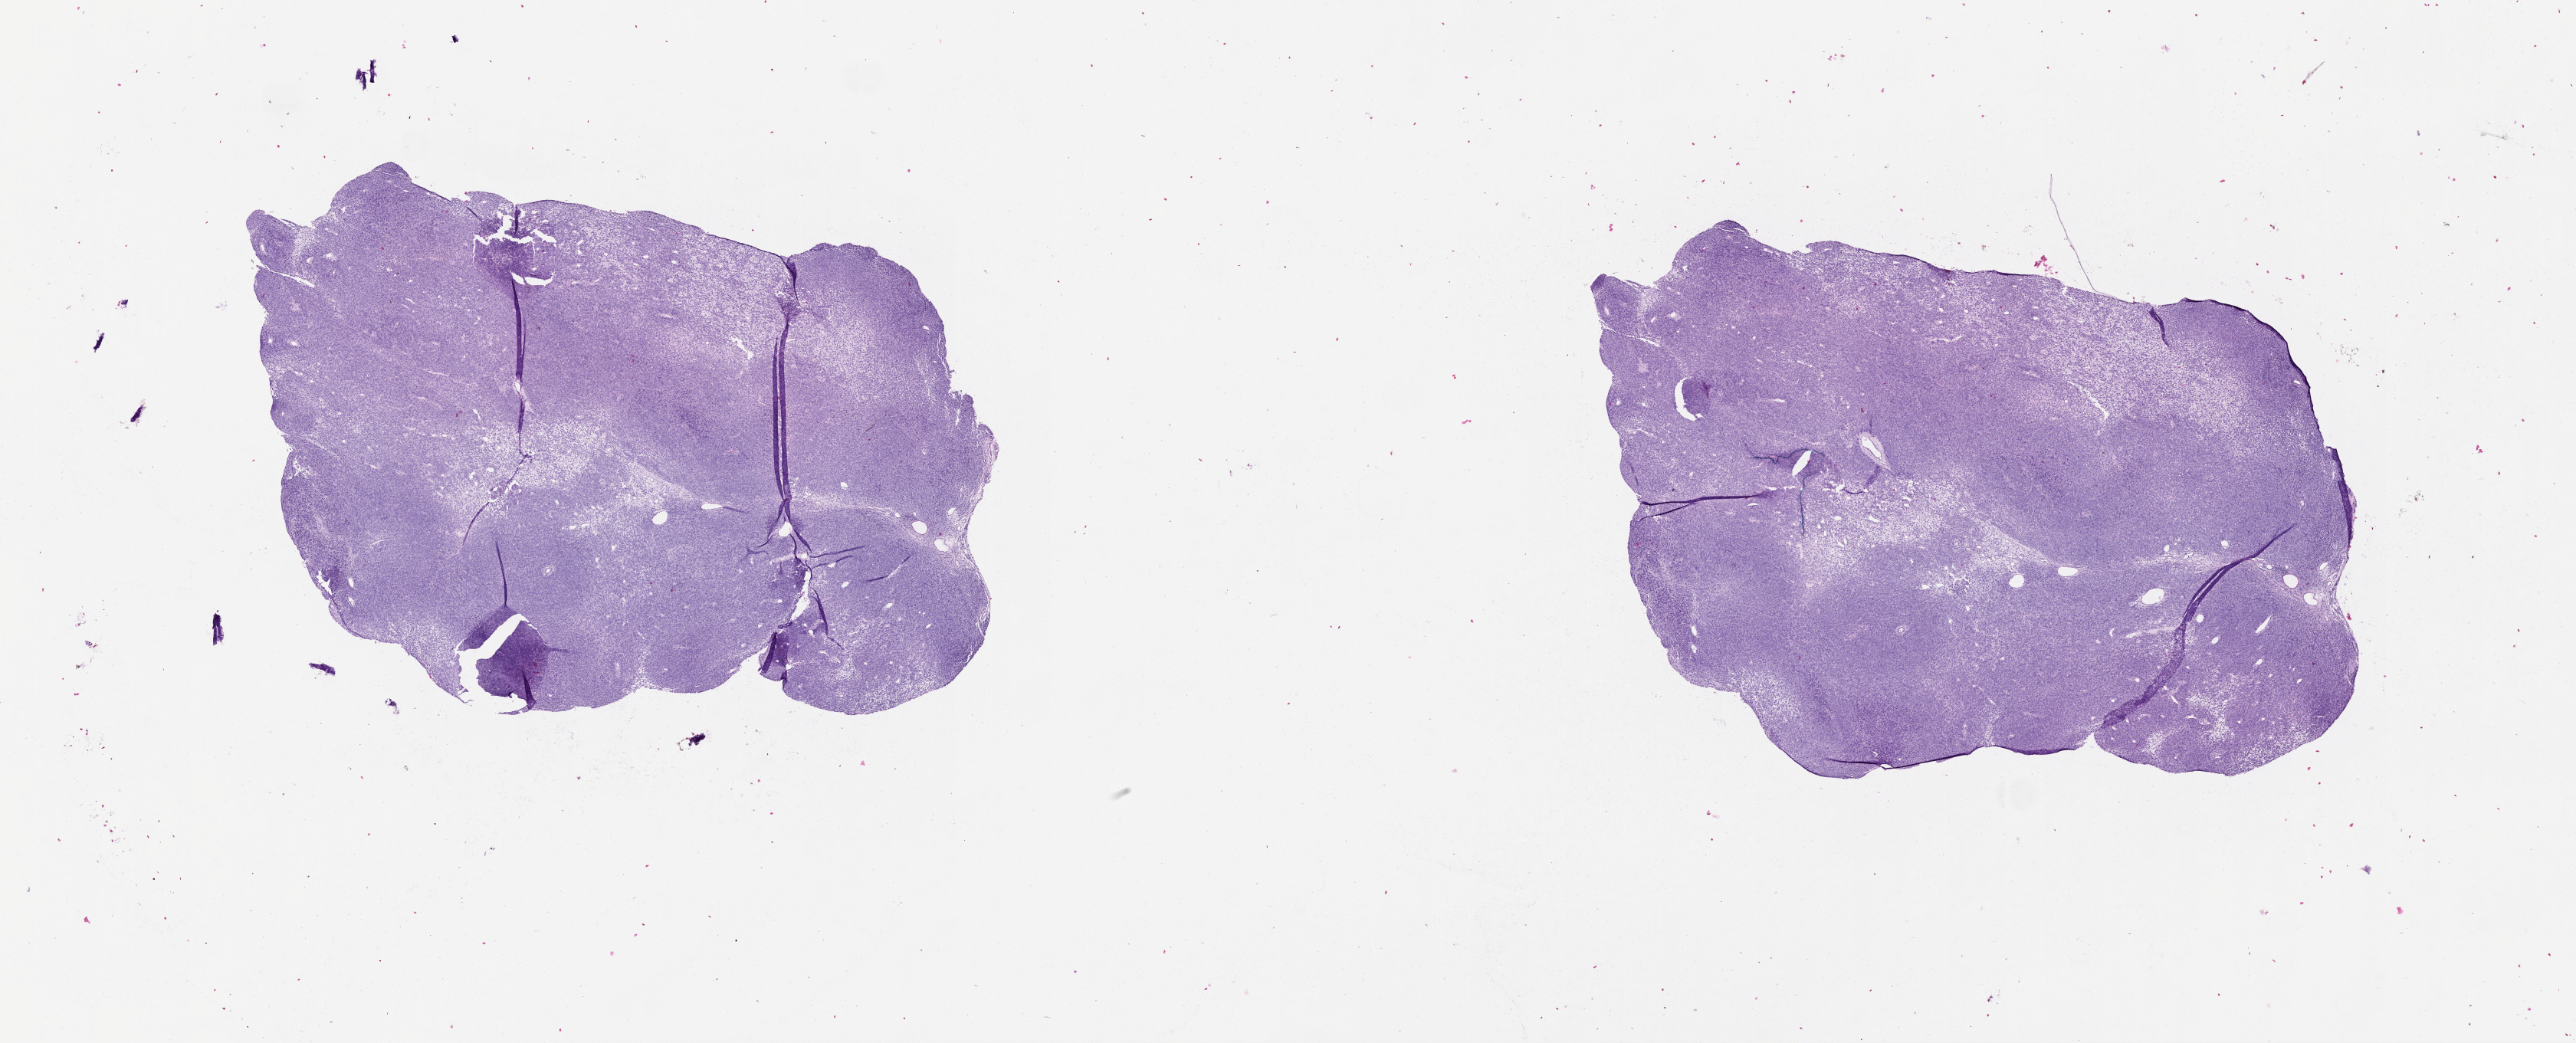
Digitized H&E tissue section (whole slide), a low-resolution overview of the entire scanned area, about 27.1 x 11.0 mm (acquisition: 20x scan). Tumour tissue sample, sampled site: lymph node. 72-year-old male patient. Composition of this section per pathologist review: tumour nuclei 80%, necrosis 0%.
* this section: metastatic tumour tissue
* patient diagnosis: Malignant melanoma, NOS